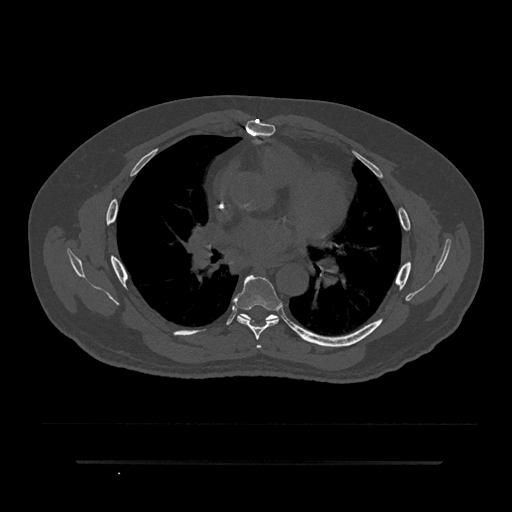
CT including the spine, one axial slice. Position 513 of 797 along the scan axis. Reconstruction kernel Br40s/3. Bone window (W 1800 / L 400 HU). 512 × 512 image matrix, field of view 464 × 464 mm. Male patient, age 59 years. From the clinical record (not read from this slice): primary cancer: bile ducts; vertebrae with lytic lesions (as recorded): T10.
Structures marked on this image (semi-automatically segmented with operator editing):
- T5 vertebra: bounding box [x1, y1, x2, y2] px = [256, 345, 261, 348]
- T6 vertebra: [233, 274, 282, 340]
- T7 vertebra: [241, 314, 276, 322]